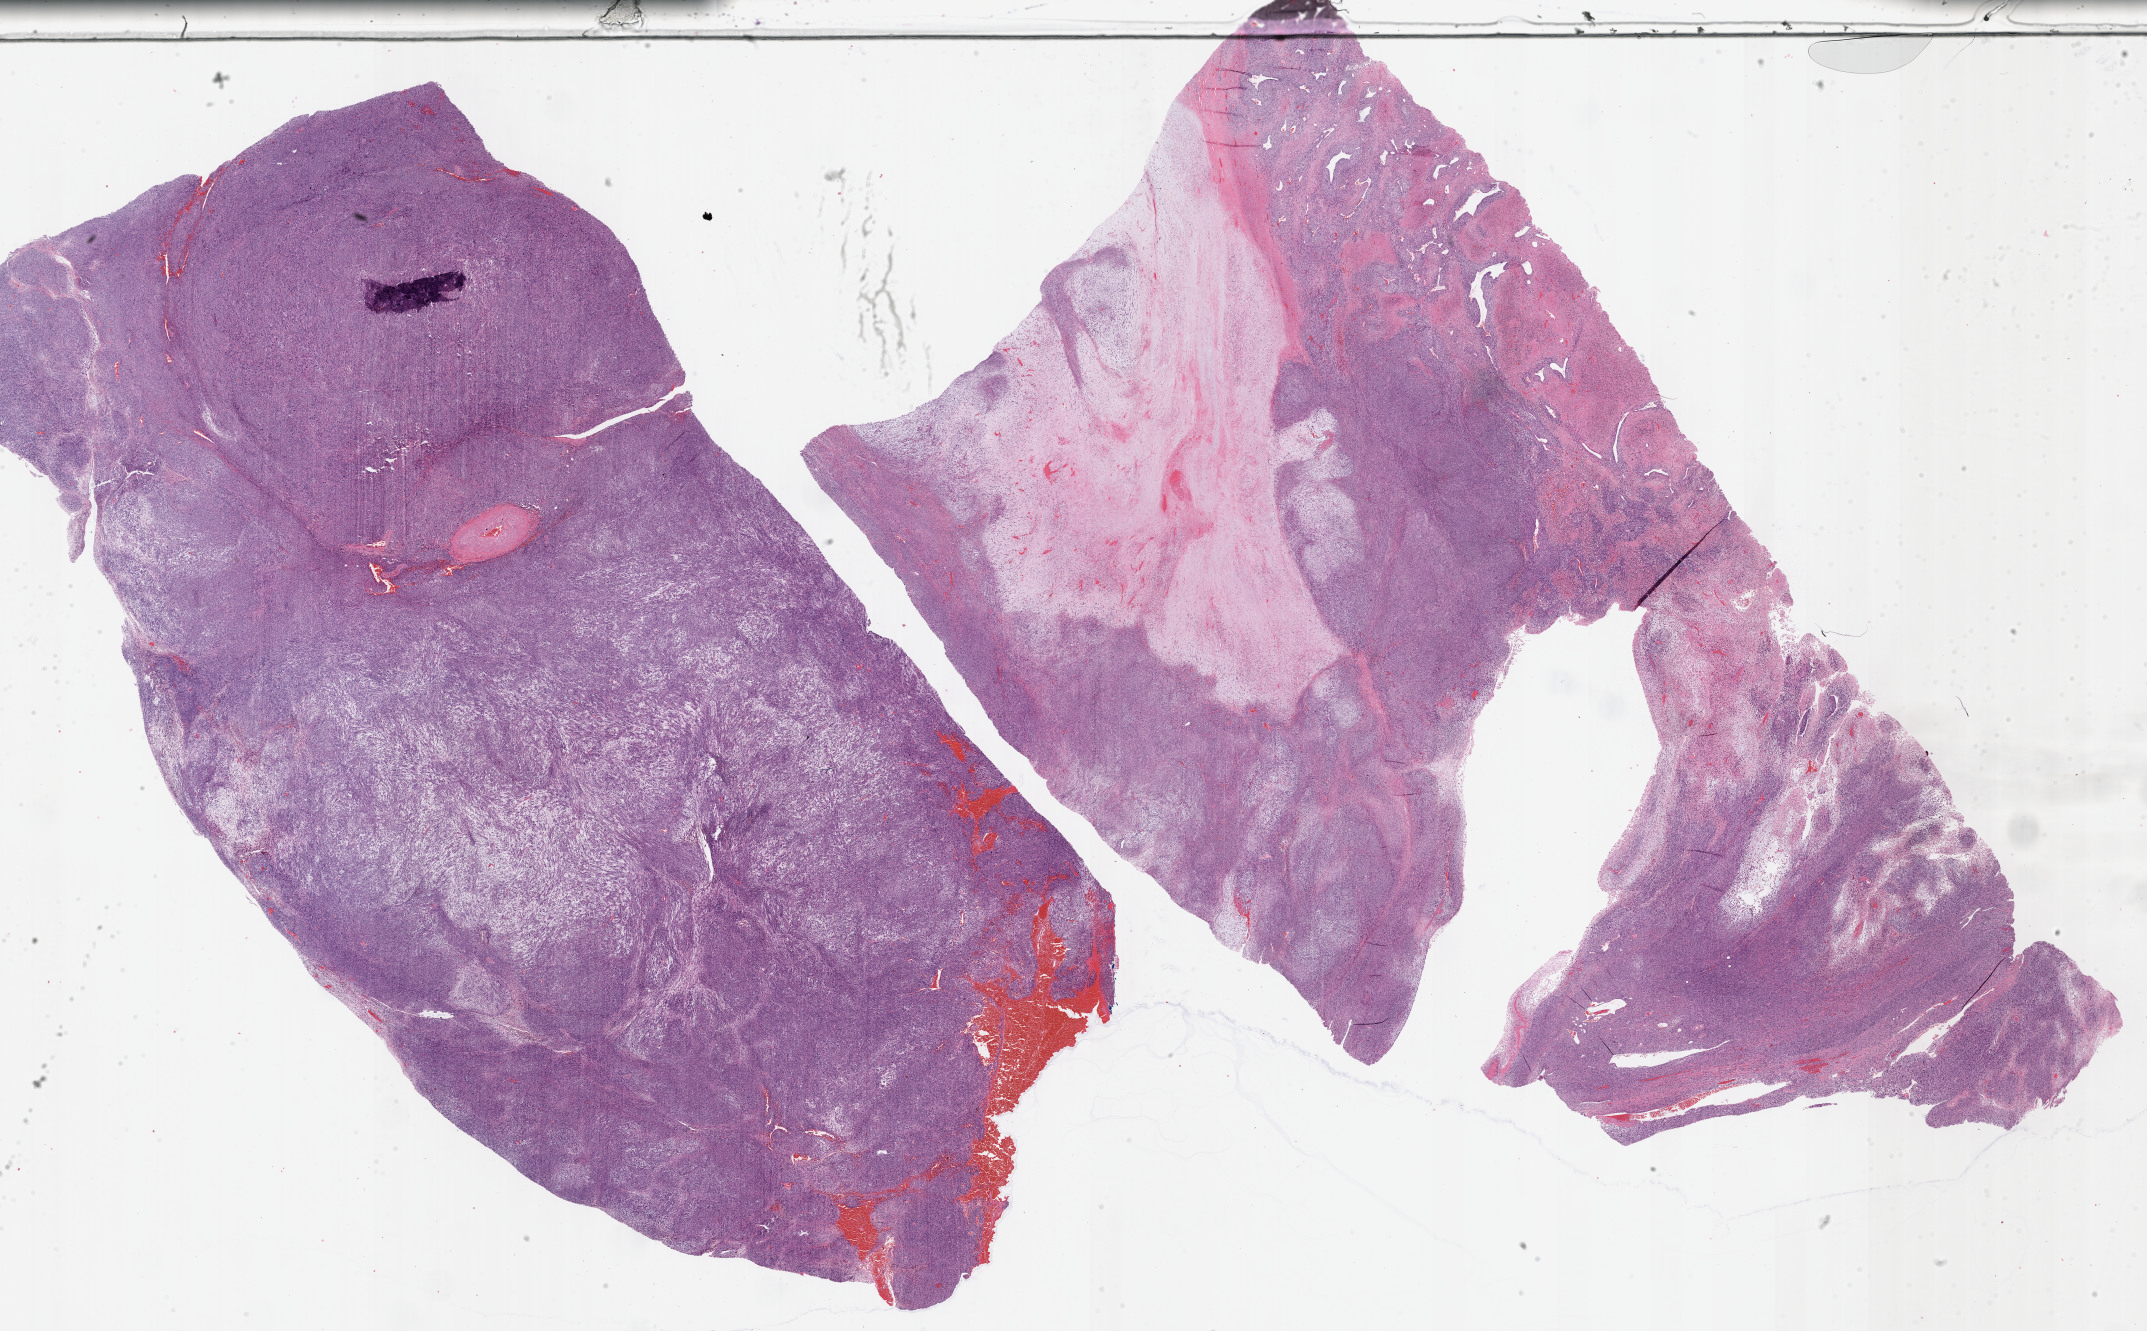
H&E whole-slide image — a low-resolution overview of the entire scanned area, about 34.7 x 21.5 mm; formalin-fixed paraffin-embedded (FFPE) diagnostic section; sample: primary tumour, connective, subcutaneous and other soft tissues. Patient: female, age at initial diagnosis 70 years.
Diagnosis: Undifferentiated sarcoma (connective, subcutaneous and other soft tissues of lower limb and hip).